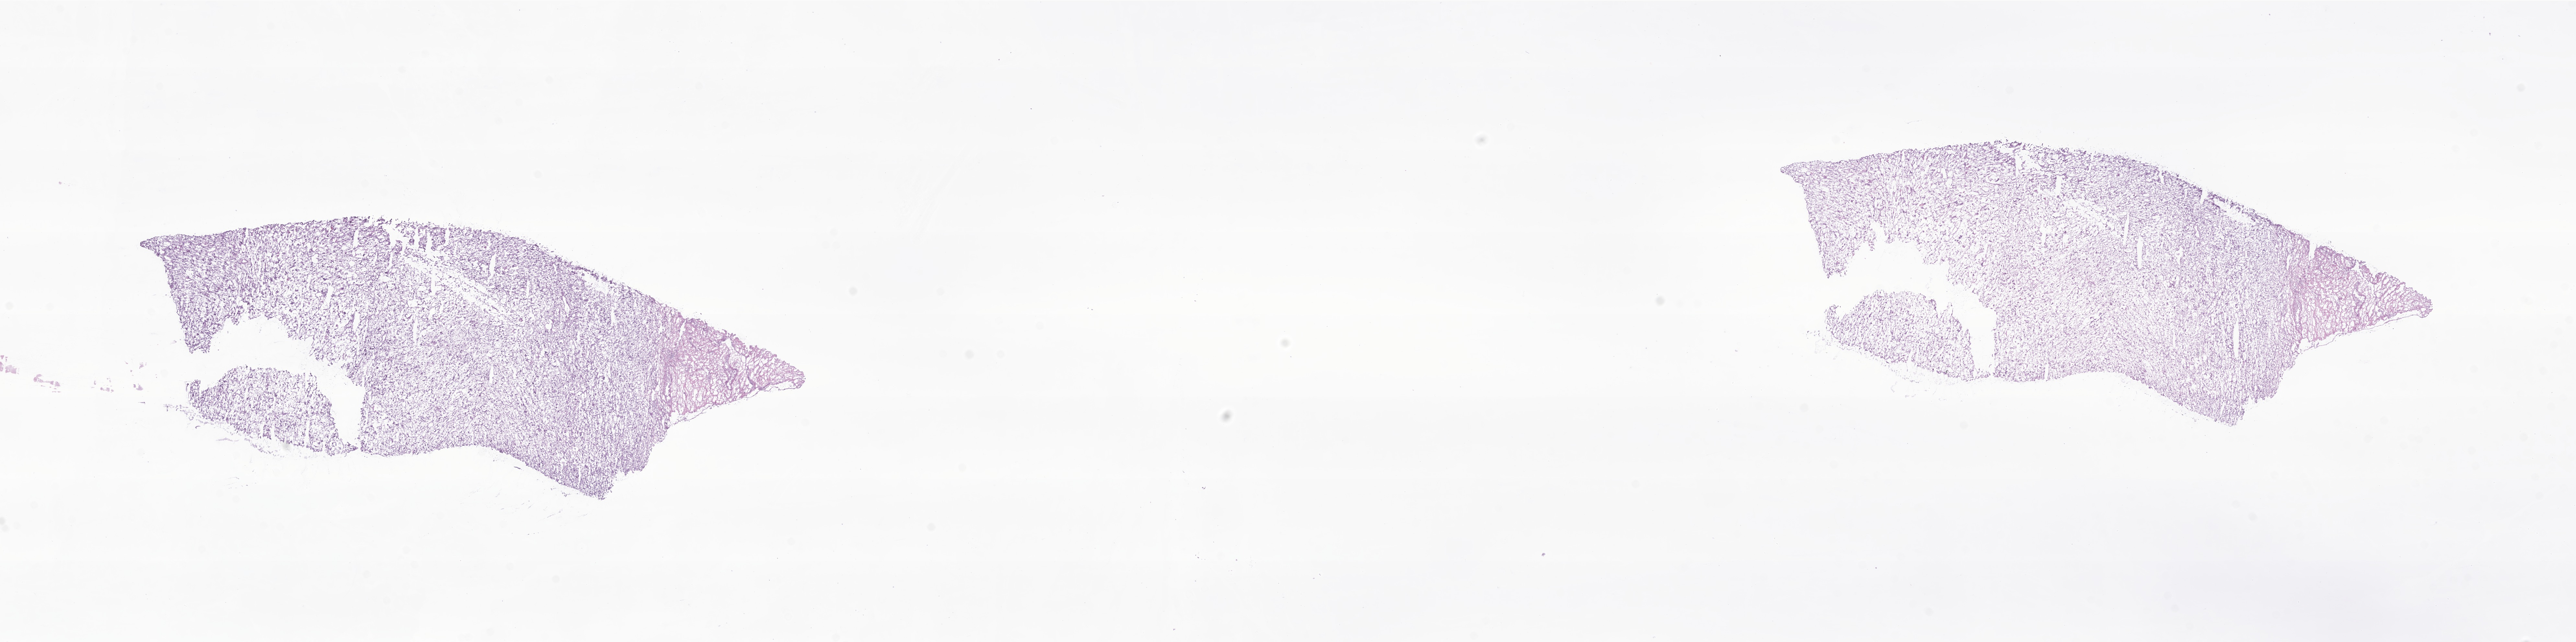
Whole-slide image, haematoxylin and eosin stain of tumor tissue from the liver, whole scanned area (about 33.5 x 8.4 mm) shown as a low-resolution overview. Frozen section (OCT-embedded). Patient: male, age 166 months (13 years 10 months).
Recorded diagnosis: Embryonal sarcoma.